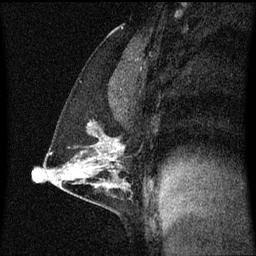
Breast MRI (dynamic contrast-enhanced), one sagittal slice; dynamic contrast-enhanced series, image 2 of 3 at this slice position (ordered by acquisition); 1.5 T; TE 4.2 ms, TR 8.4 ms; 2 mm slice thickness; 256 × 256 image matrix, field of view 200 × 200 mm. Female patient, age 40 years. Case-level facts recorded for this patient, not image findings: setting: breast cancer imaged before/during neoadjuvant chemotherapy; receptor status: triple-negative.
Annotated regions visible in this slice (semi-automatically segmented with operator editing):
- analysis volume of interest (the breast-tissue region the enhancement analysis was run in; not a lesion): bounding box <43,120,132,195> (left, top, right, bottom; pixels)
- tumour enhancement mask (voxels above the 70 % enhancement threshold inside the analysis volume of interest): <112,144,124,153>